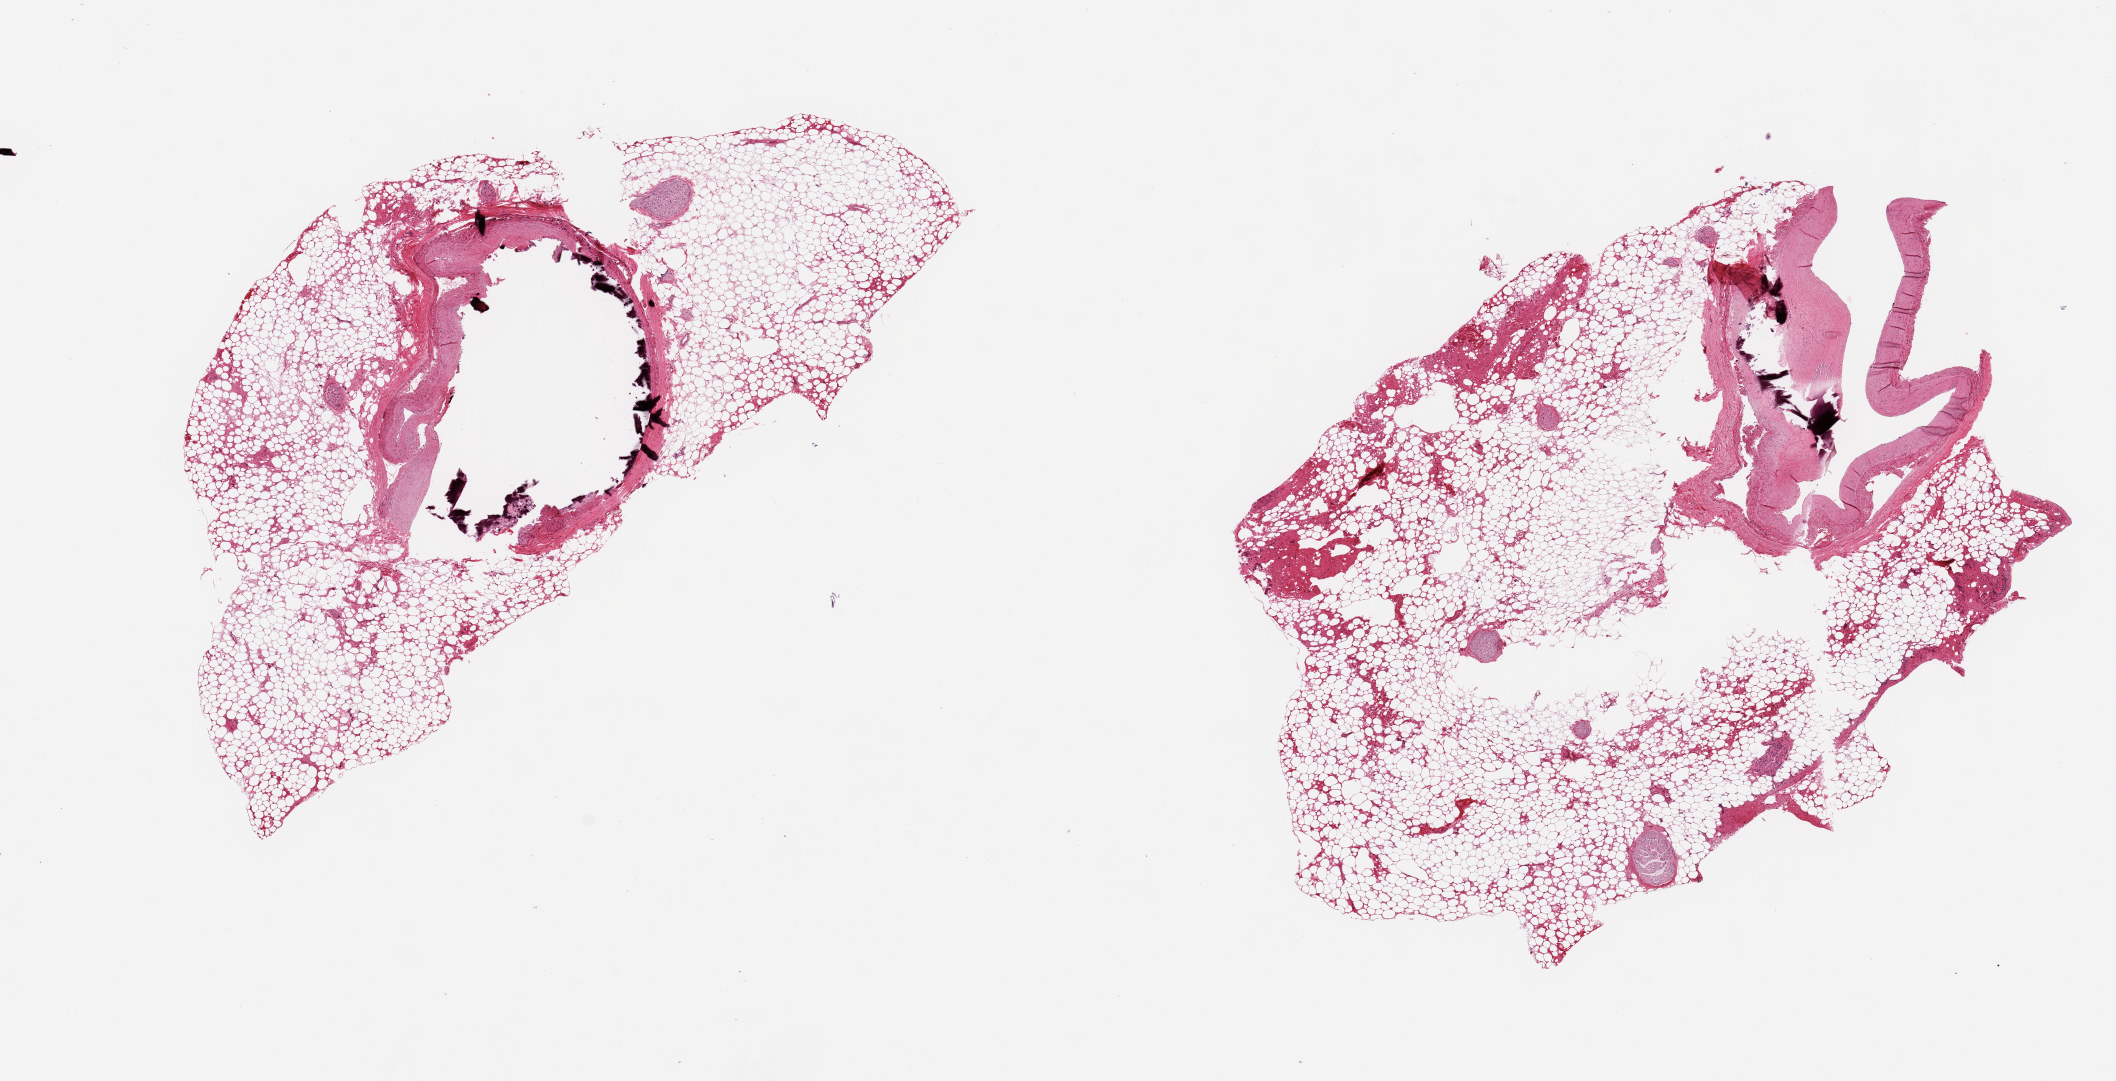
Whole-slide image, haematoxylin and eosin stain — low-resolution overview of the scanned area, about 16.7 x 8.5 mm (acquisition: 20x scan); PAXgene-fixed paraffin-embedded (PFPE) section; target tissue: coronary artery; tissue donor sample.
Reviewer comment on this tissue sample: 2 ~2mm artery. Dense calcification. Note: aliquots surrounded by up to2.5-5mm layer of fat (60% of total aliquot).